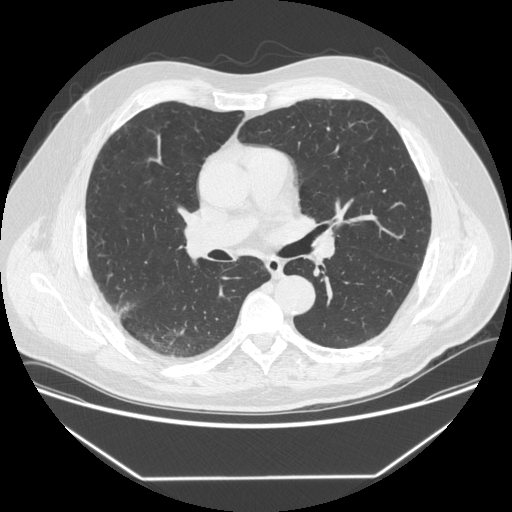
Axial slice from a low-dose chest CT screening exam; baseline screening round; lung window (W 1500 / L -600 HU); 120 kVp; 512 × 512 image matrix. Male participant, aged 64 years at enrolment.
- Lesion marked by an expert reader, bounding box <100,298,141,328> (left, top, right, bottom; pixels).
- Reader record for this screening exam (exam-level; its link to the box is not recorded): non-calcified nodule or mass ≥4 mm, right upper lobe, 12 × 12 mm, smooth margins, soft tissue attenuation.
- Official screen result: positive, change unspecified: nodule(s) >= 4 mm or enlarging nodule(s), mass(es), or other non-specific abnormalities suspicious for lung cancer.
- Later outcome: lung cancer diagnosed 92 days after this screen — adenocarcinoma, NOS, right upper lobe, poorly differentiated (G3), stage IIIB (AJCC 6th edition), 15 mm at pathology.